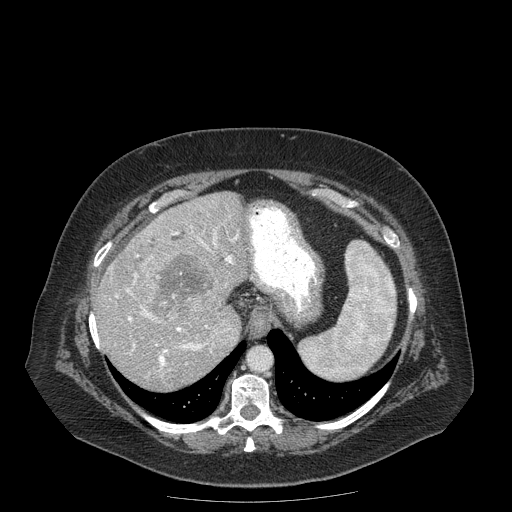
Contrast-enhanced abdominal CT (liver protocol), one axial slice; slice 139 of 204 in the series (ordered by position); reconstruction kernel STANDARD; 120 kVp; soft-tissue window (W 400 / L 40 HU); 512 × 512 image matrix, field of view 440 × 440 mm. From the clinical record (not read from this slice): diagnosis: hepatocellular carcinoma (patient treated with transarterial chemoembolisation; whether this scan precedes or follows treatment is not stated here); TNM stage (as recorded): Stage-IIIB; Child-Pugh class: A.
Annotated regions visible in this slice (semi-automatic segmentation, software-assisted and operator-edited):
- liver parenchyma outside the tumour (the mass and vessels are separate outlines, so this box may not span the whole liver): bounding box <94,192,248,390> (left, top, right, bottom; pixels)
- mass: <141,239,226,322>
- liver vessels: <115,216,239,371>